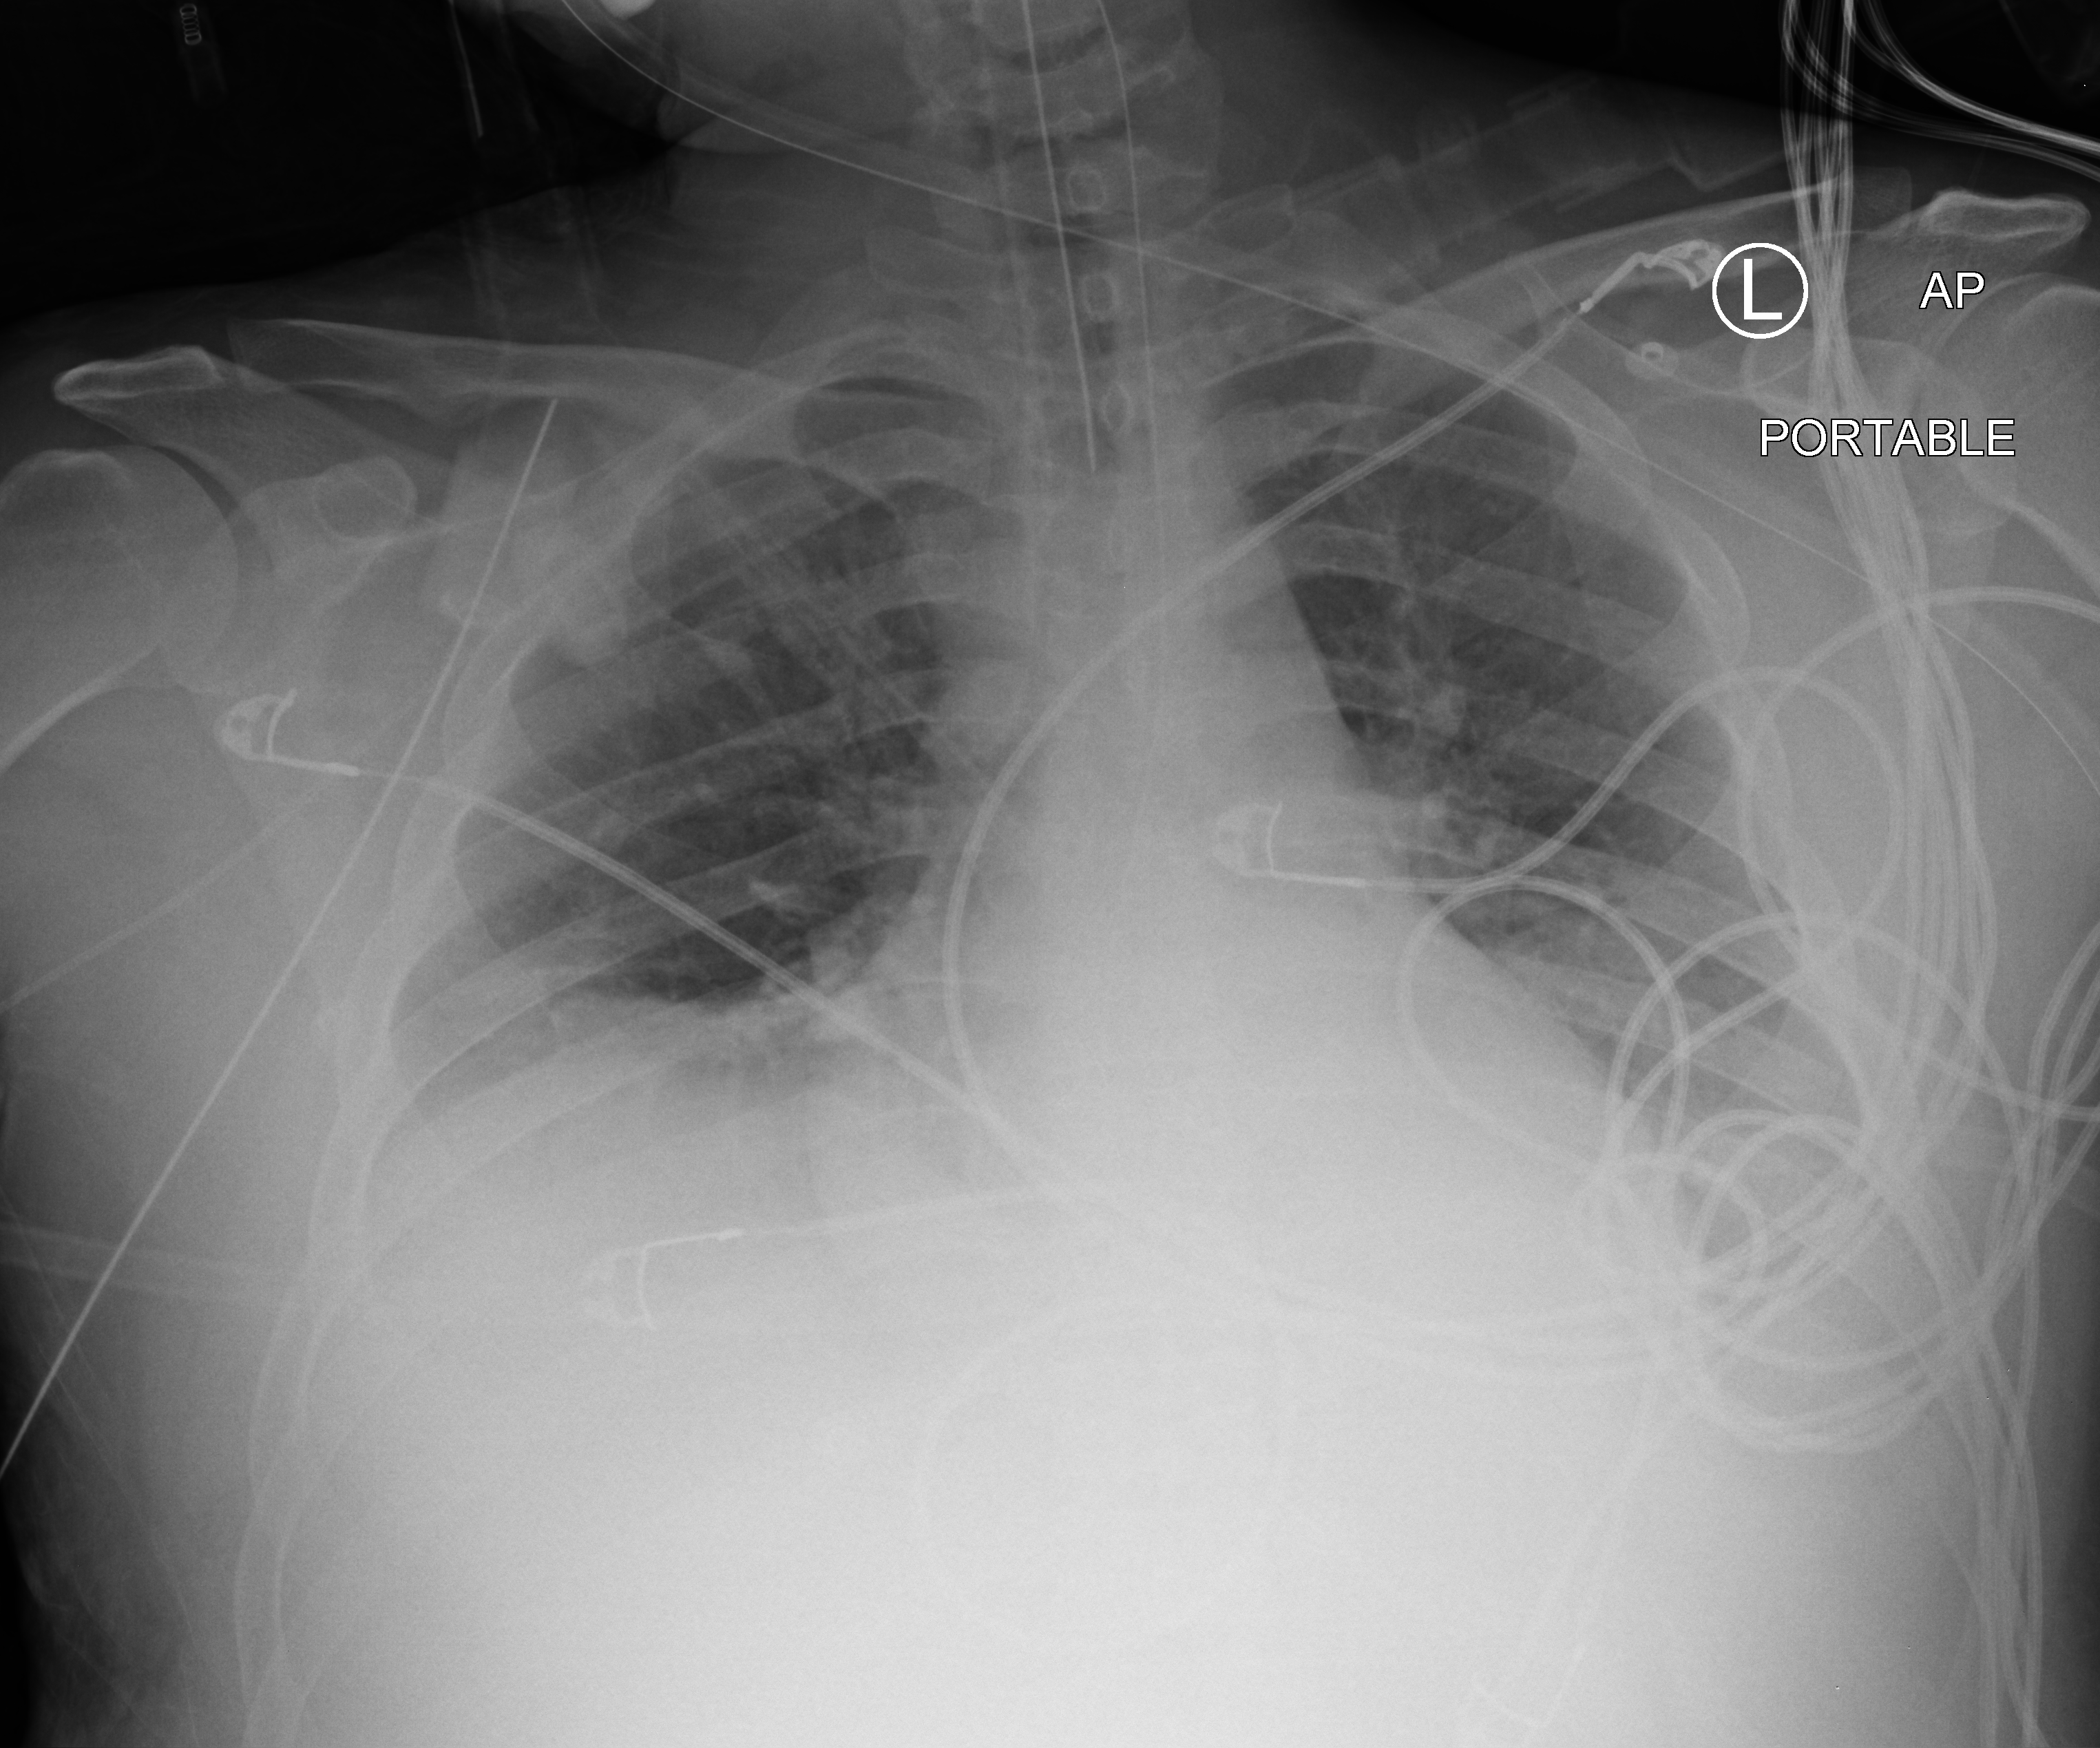
Chest X-ray (portable), anteroposterior (AP) projection. Male patient hospitalised with COVID-19, age 18–59 years.
Hospital-stay facts (about this admission, not read from this image; timing relative to this image not recorded): COPD (admission record): no; admitted to intensive care during this hospital stay: yes; mechanically ventilated during this hospital stay: yes.